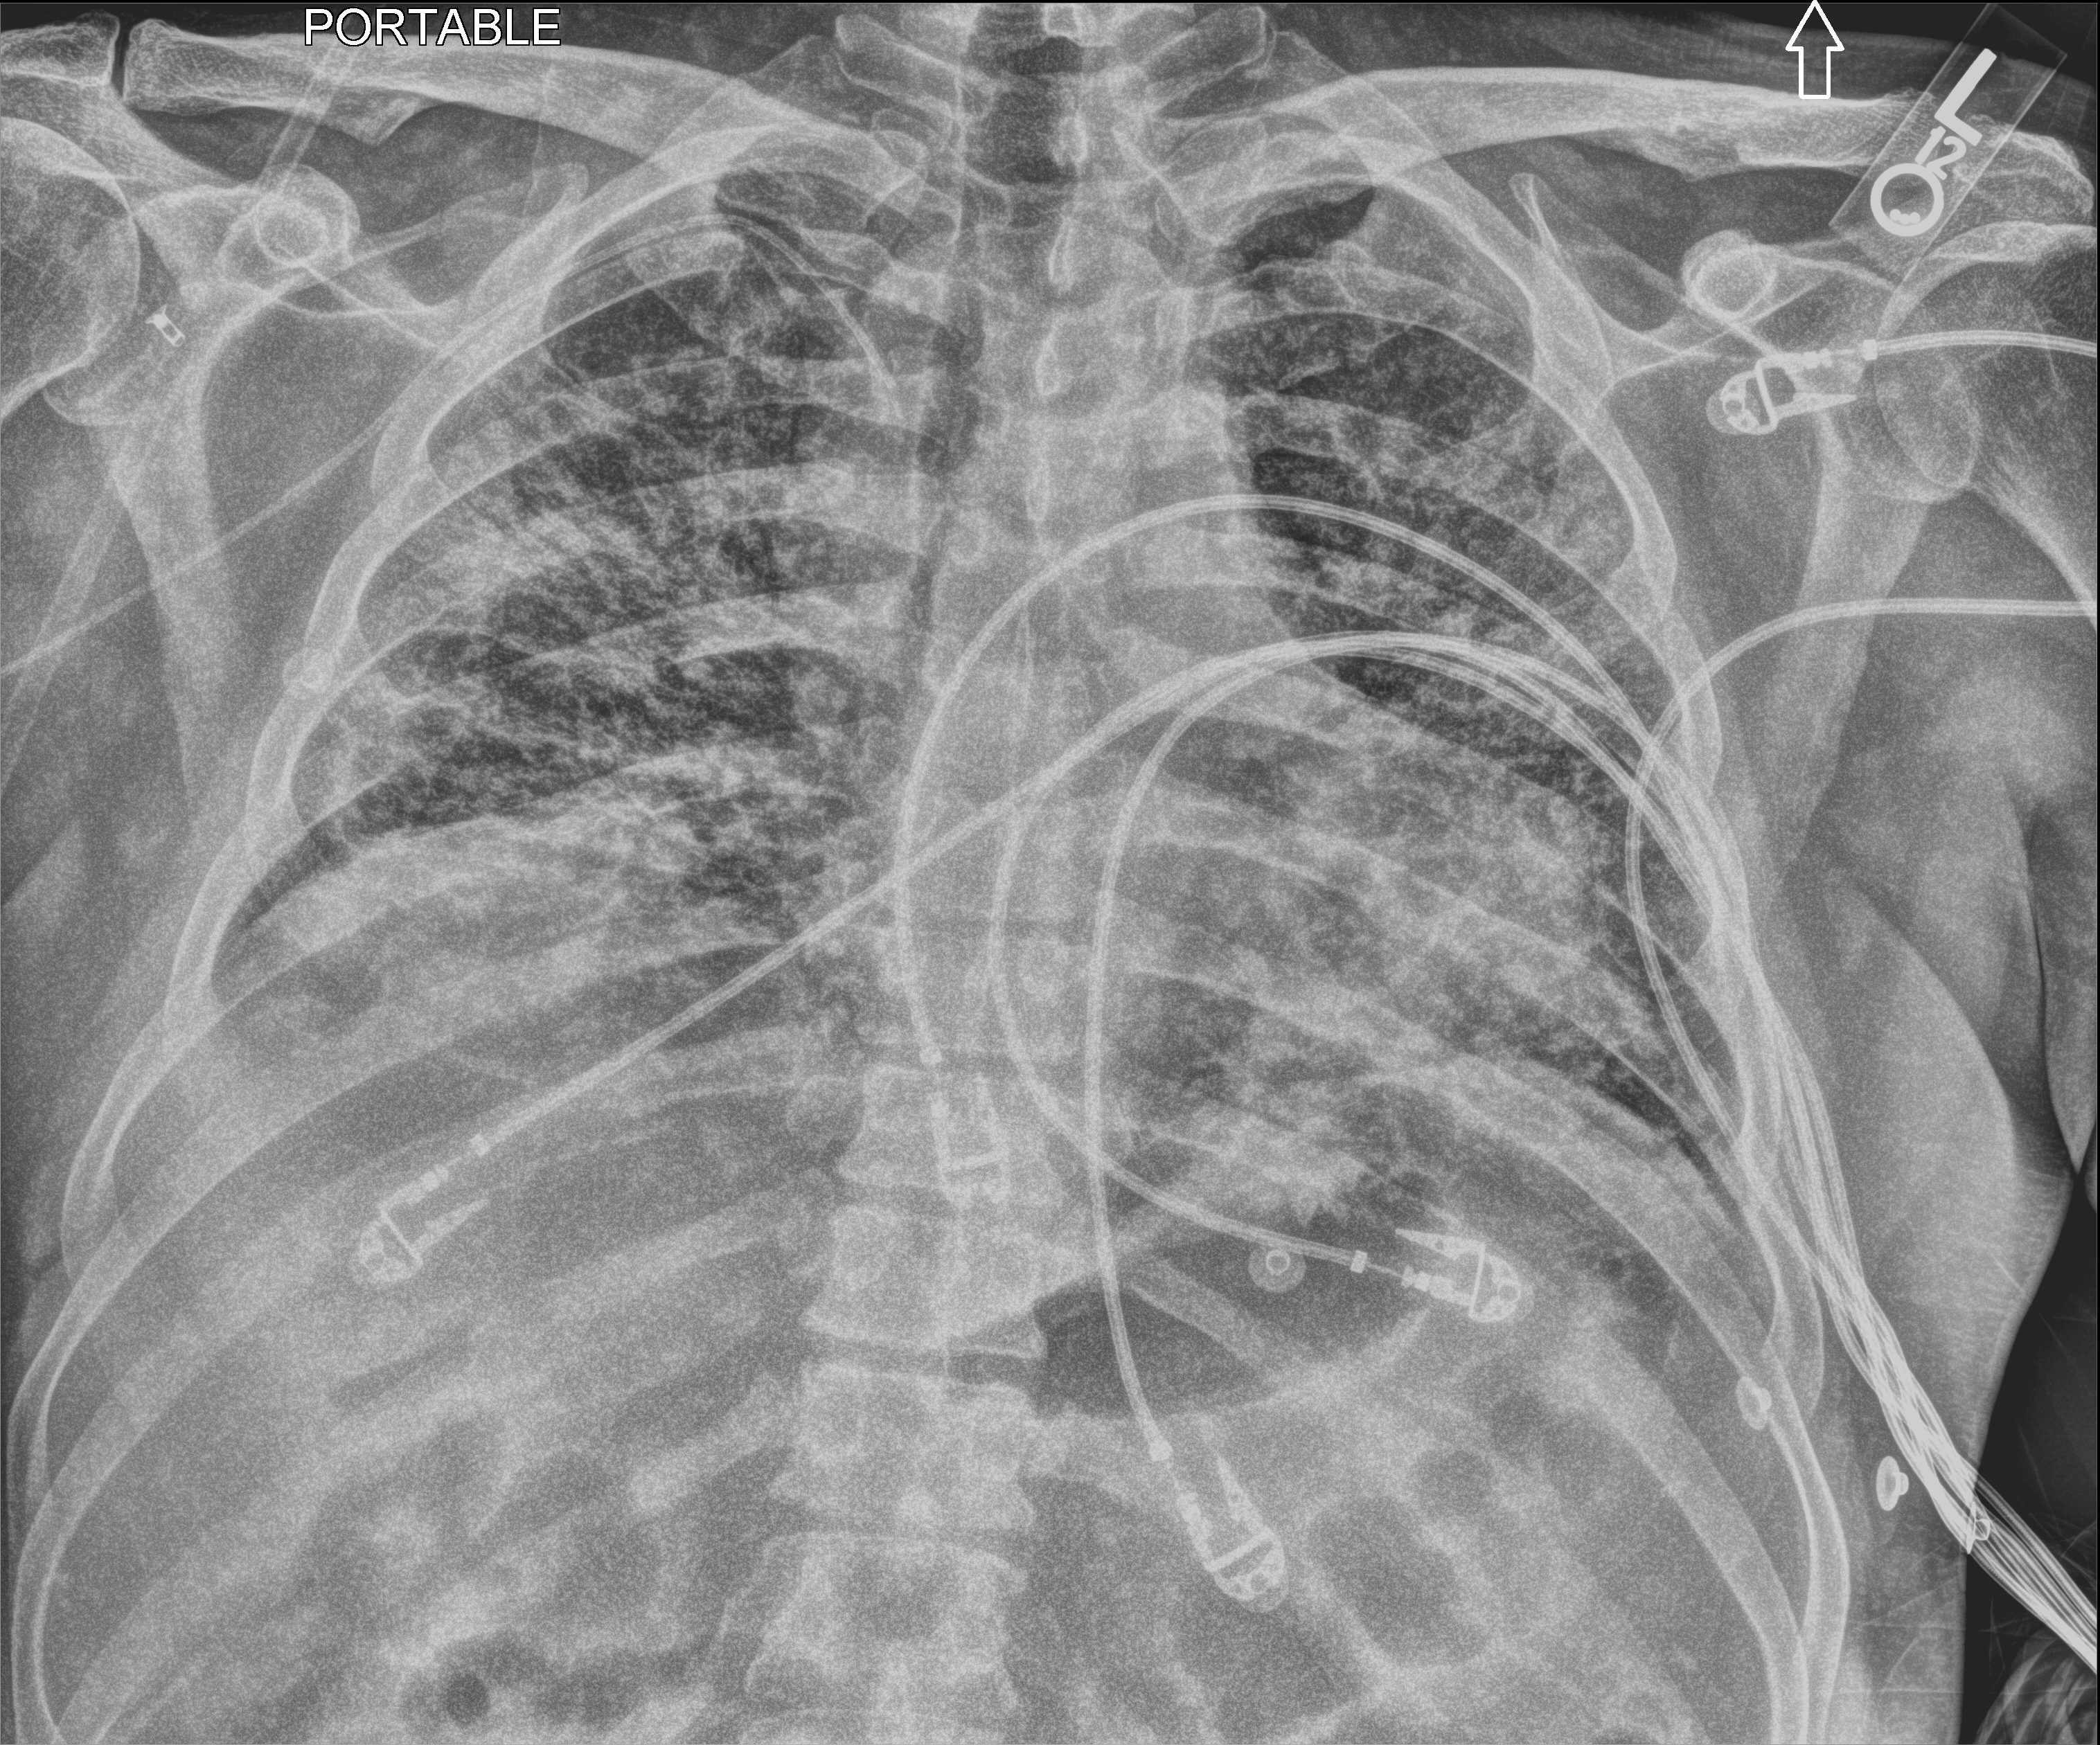
Chest X-ray (portable). Patient hospitalised with COVID-19; male, aged 18–59 years.
Hospital-stay facts (about this admission, not read from this image; timing relative to this image not recorded): mechanically ventilated during this hospital stay: yes.